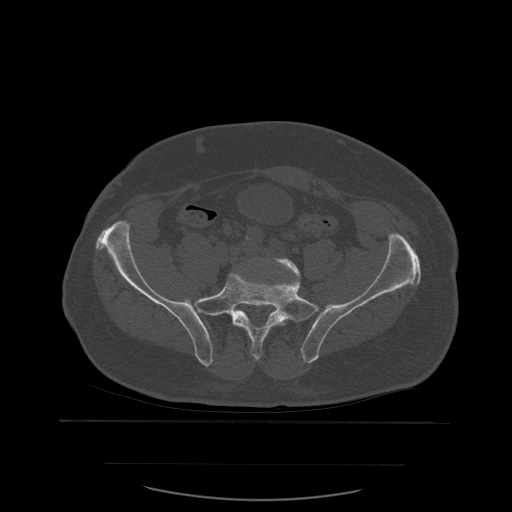
CT including the spine, one axial slice; position 119 of 590 along the scan axis; bone window (W 1800 / L 400 HU); 1.25 mm slice thickness; 512 × 512 image matrix. Patient age 71 years. From the clinical record (not read from this slice): primary cancer: lung; vertebrae with lytic lesions (as recorded): T1, T2, L5, S1.
Annotated regions visible in this slice (semi-automatic segmentation, software-assisted and operator-edited):
- L5 vertebra: bounding box <253,258,301,357> (left, top, right, bottom; pixels)